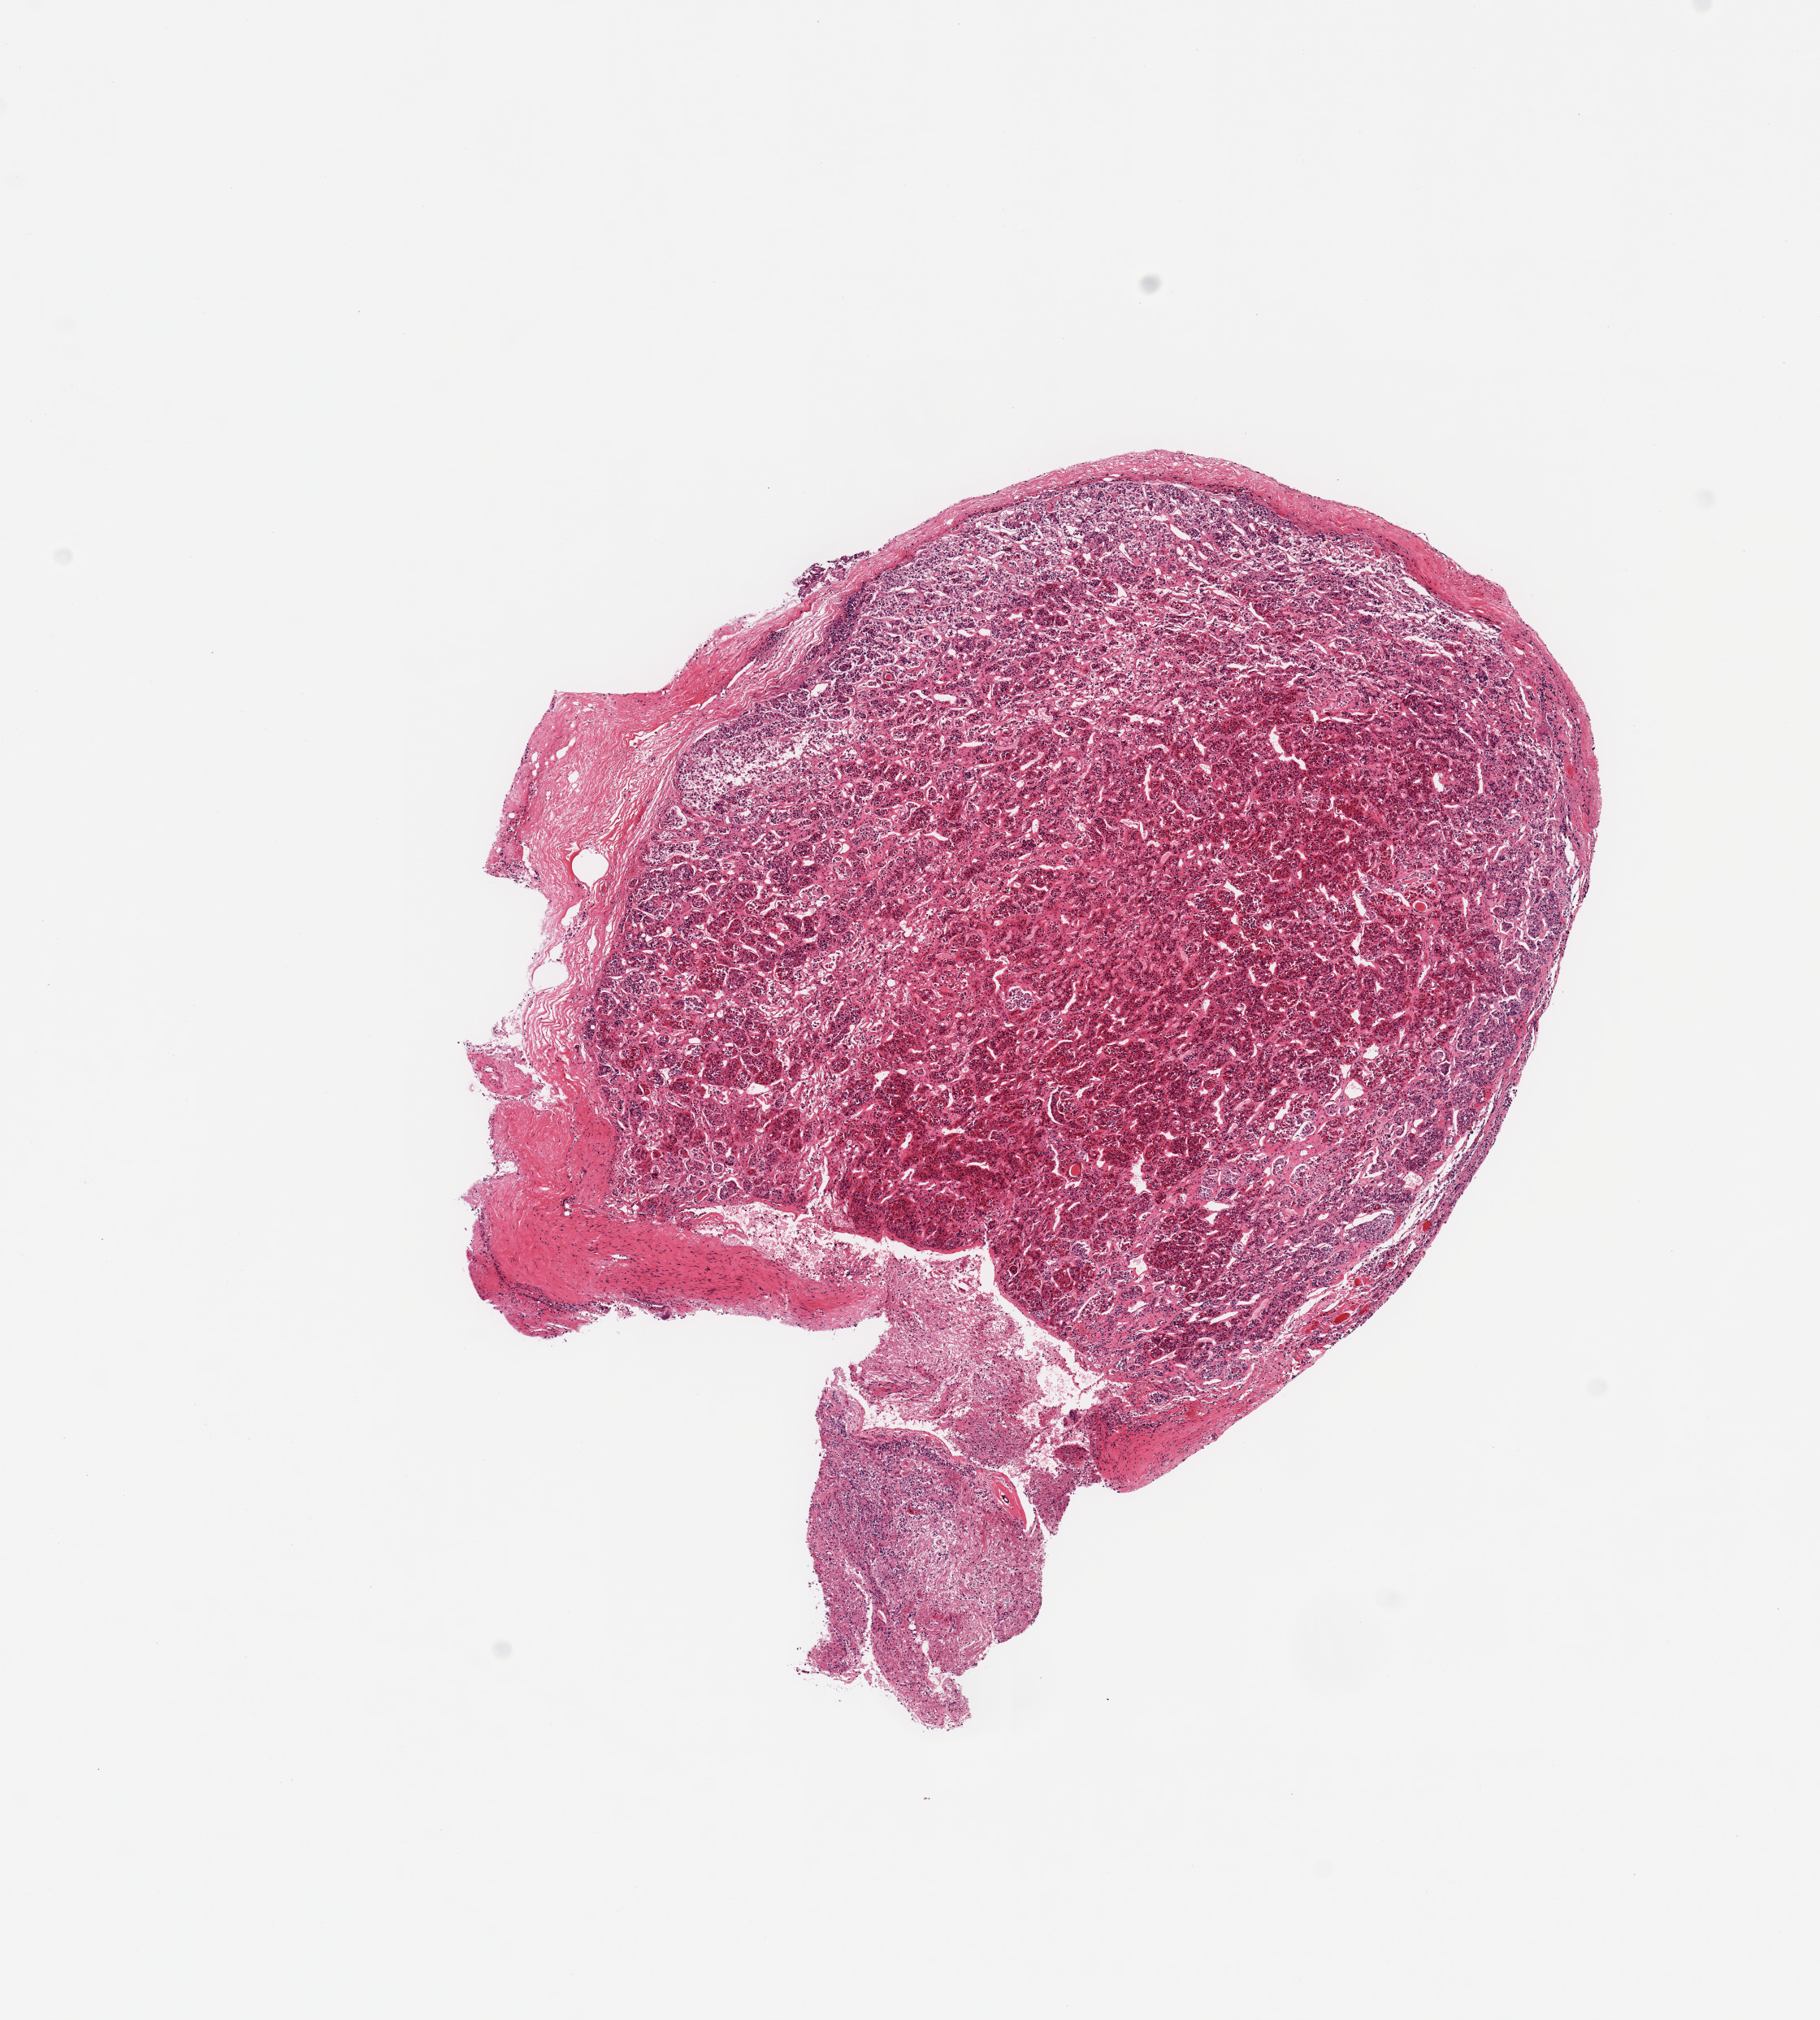
Digitized H&E-stained section, a low-resolution overview of the entire scanned area, about 8.9 x 9.8 mm (from a 20x scan). PAXgene-fixed, paraffin-embedded tissue. Sampled site (target tissue): pituitary. Tissue donor sample. Donor: male.
- review note (as recorded): 2 pieces, mainly adenohypophysis; 2mm nubbin of neurohypophysis